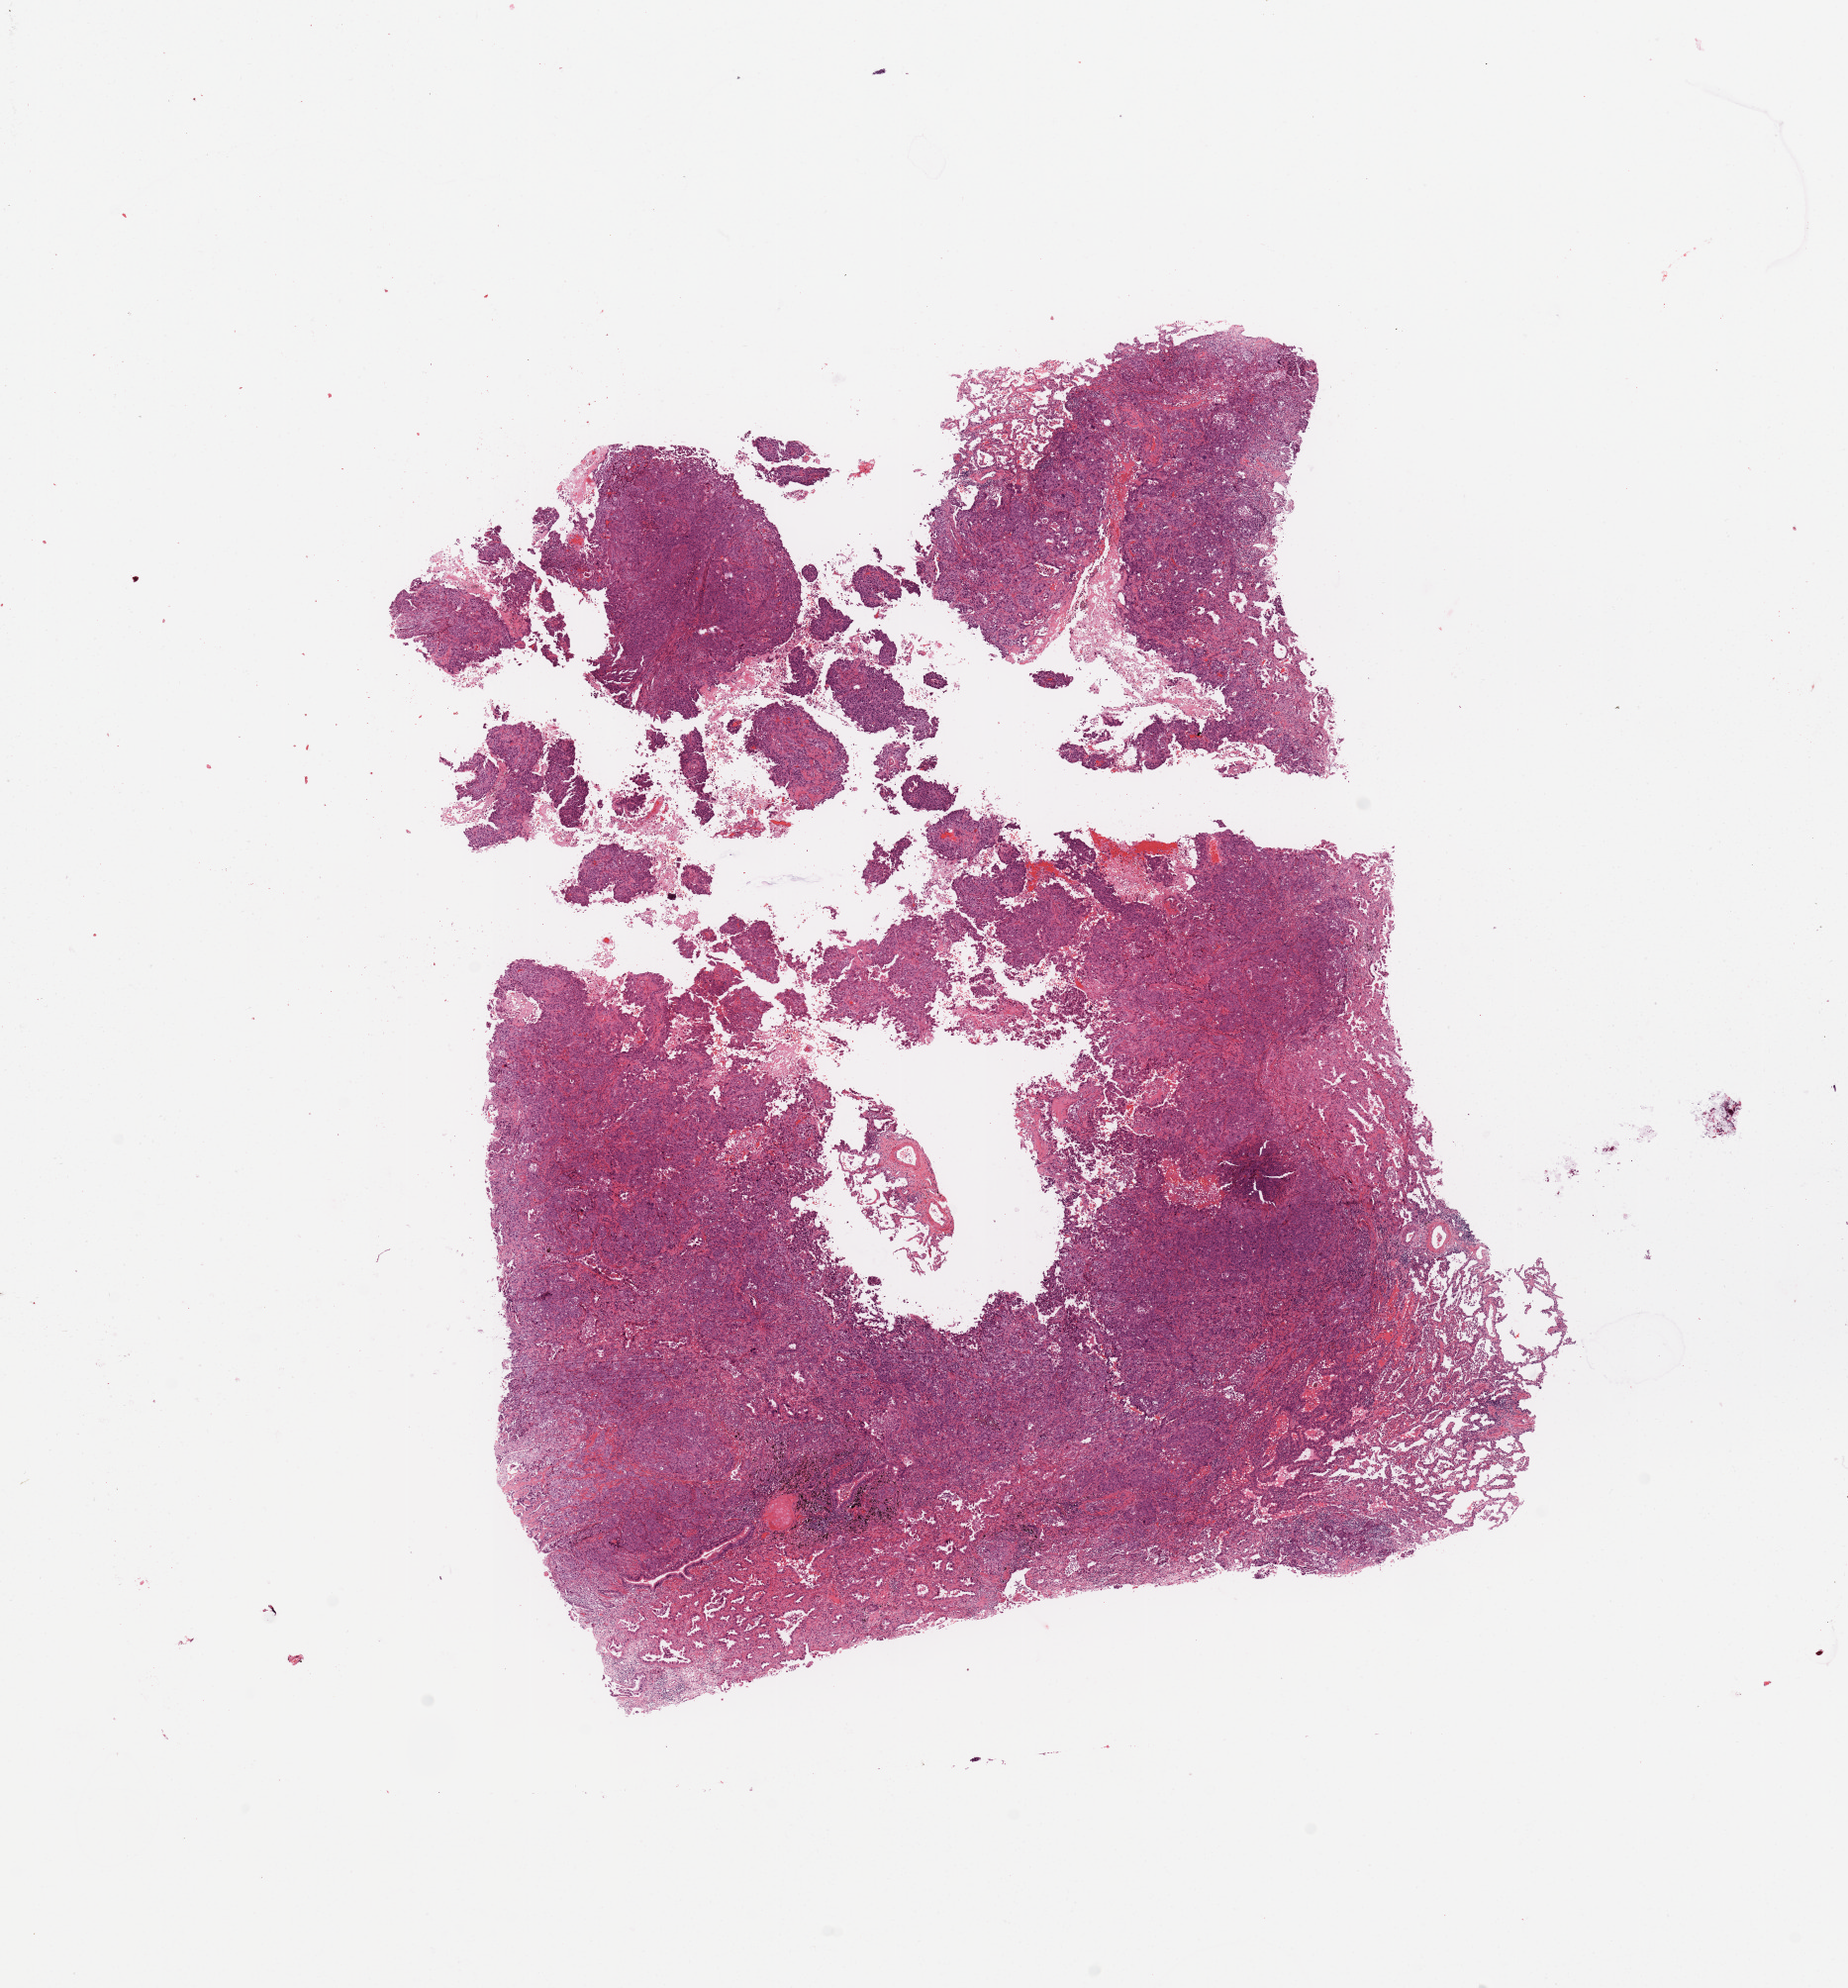
Digitized Hematoxylin and eosin (H&E) stained tissue section (whole slide), low-resolution overview of the scanned area, about 14.8 x 15.9 mm; tumour tissue sample, sampled site: lung. 57-year-old female patient. Histologic grade: G3 (poorly differentiated). Pathologist review of this section (percent, as recorded): tumour nuclei 80%, necrosis 5%.
AJCC pathologic stage: IIA. Primary tumour site (as recorded): right upper lobe. Diagnosis: Adenocarcinoma, NOS.